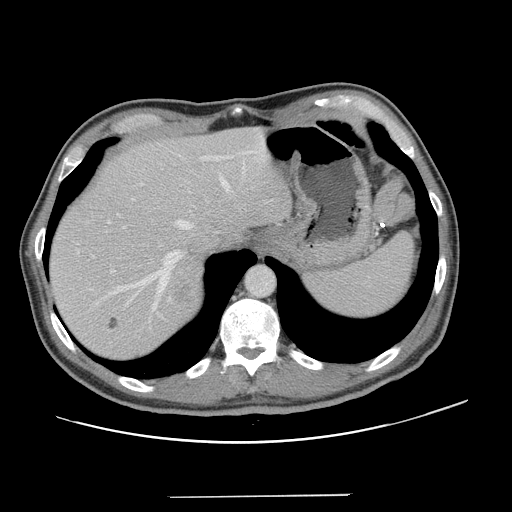
Contrast-enhanced abdominal CT, one axial slice; position 105 of 131 along the scan axis; 120 kVp; intravenous contrast given; soft-tissue window (W 400 / L 40 HU); 2.5 mm slice thickness; 512 × 512 image matrix. Male patient, age 60 years. From the clinical record (not read from this slice): diagnosis: colorectal cancer liver metastases, imaged before liver resection; multiple liver metastases: no; largest metastasis: 2.5 cm; disease in both lobes: no.
Outlined on this slice (manually delineated by an expert):
- hepatic veins: box from (x=109, y=155) to (x=230, y=311) px
- liver: (x=49, y=126)–(x=292, y=360)
- planned liver remnant (the part of the liver to remain after resection): (x=49, y=126)–(x=292, y=349)
- portal vein (with intrahepatic branches): (x=92, y=155)–(x=233, y=273)
- liver metastasis: (x=174, y=285)–(x=191, y=306)